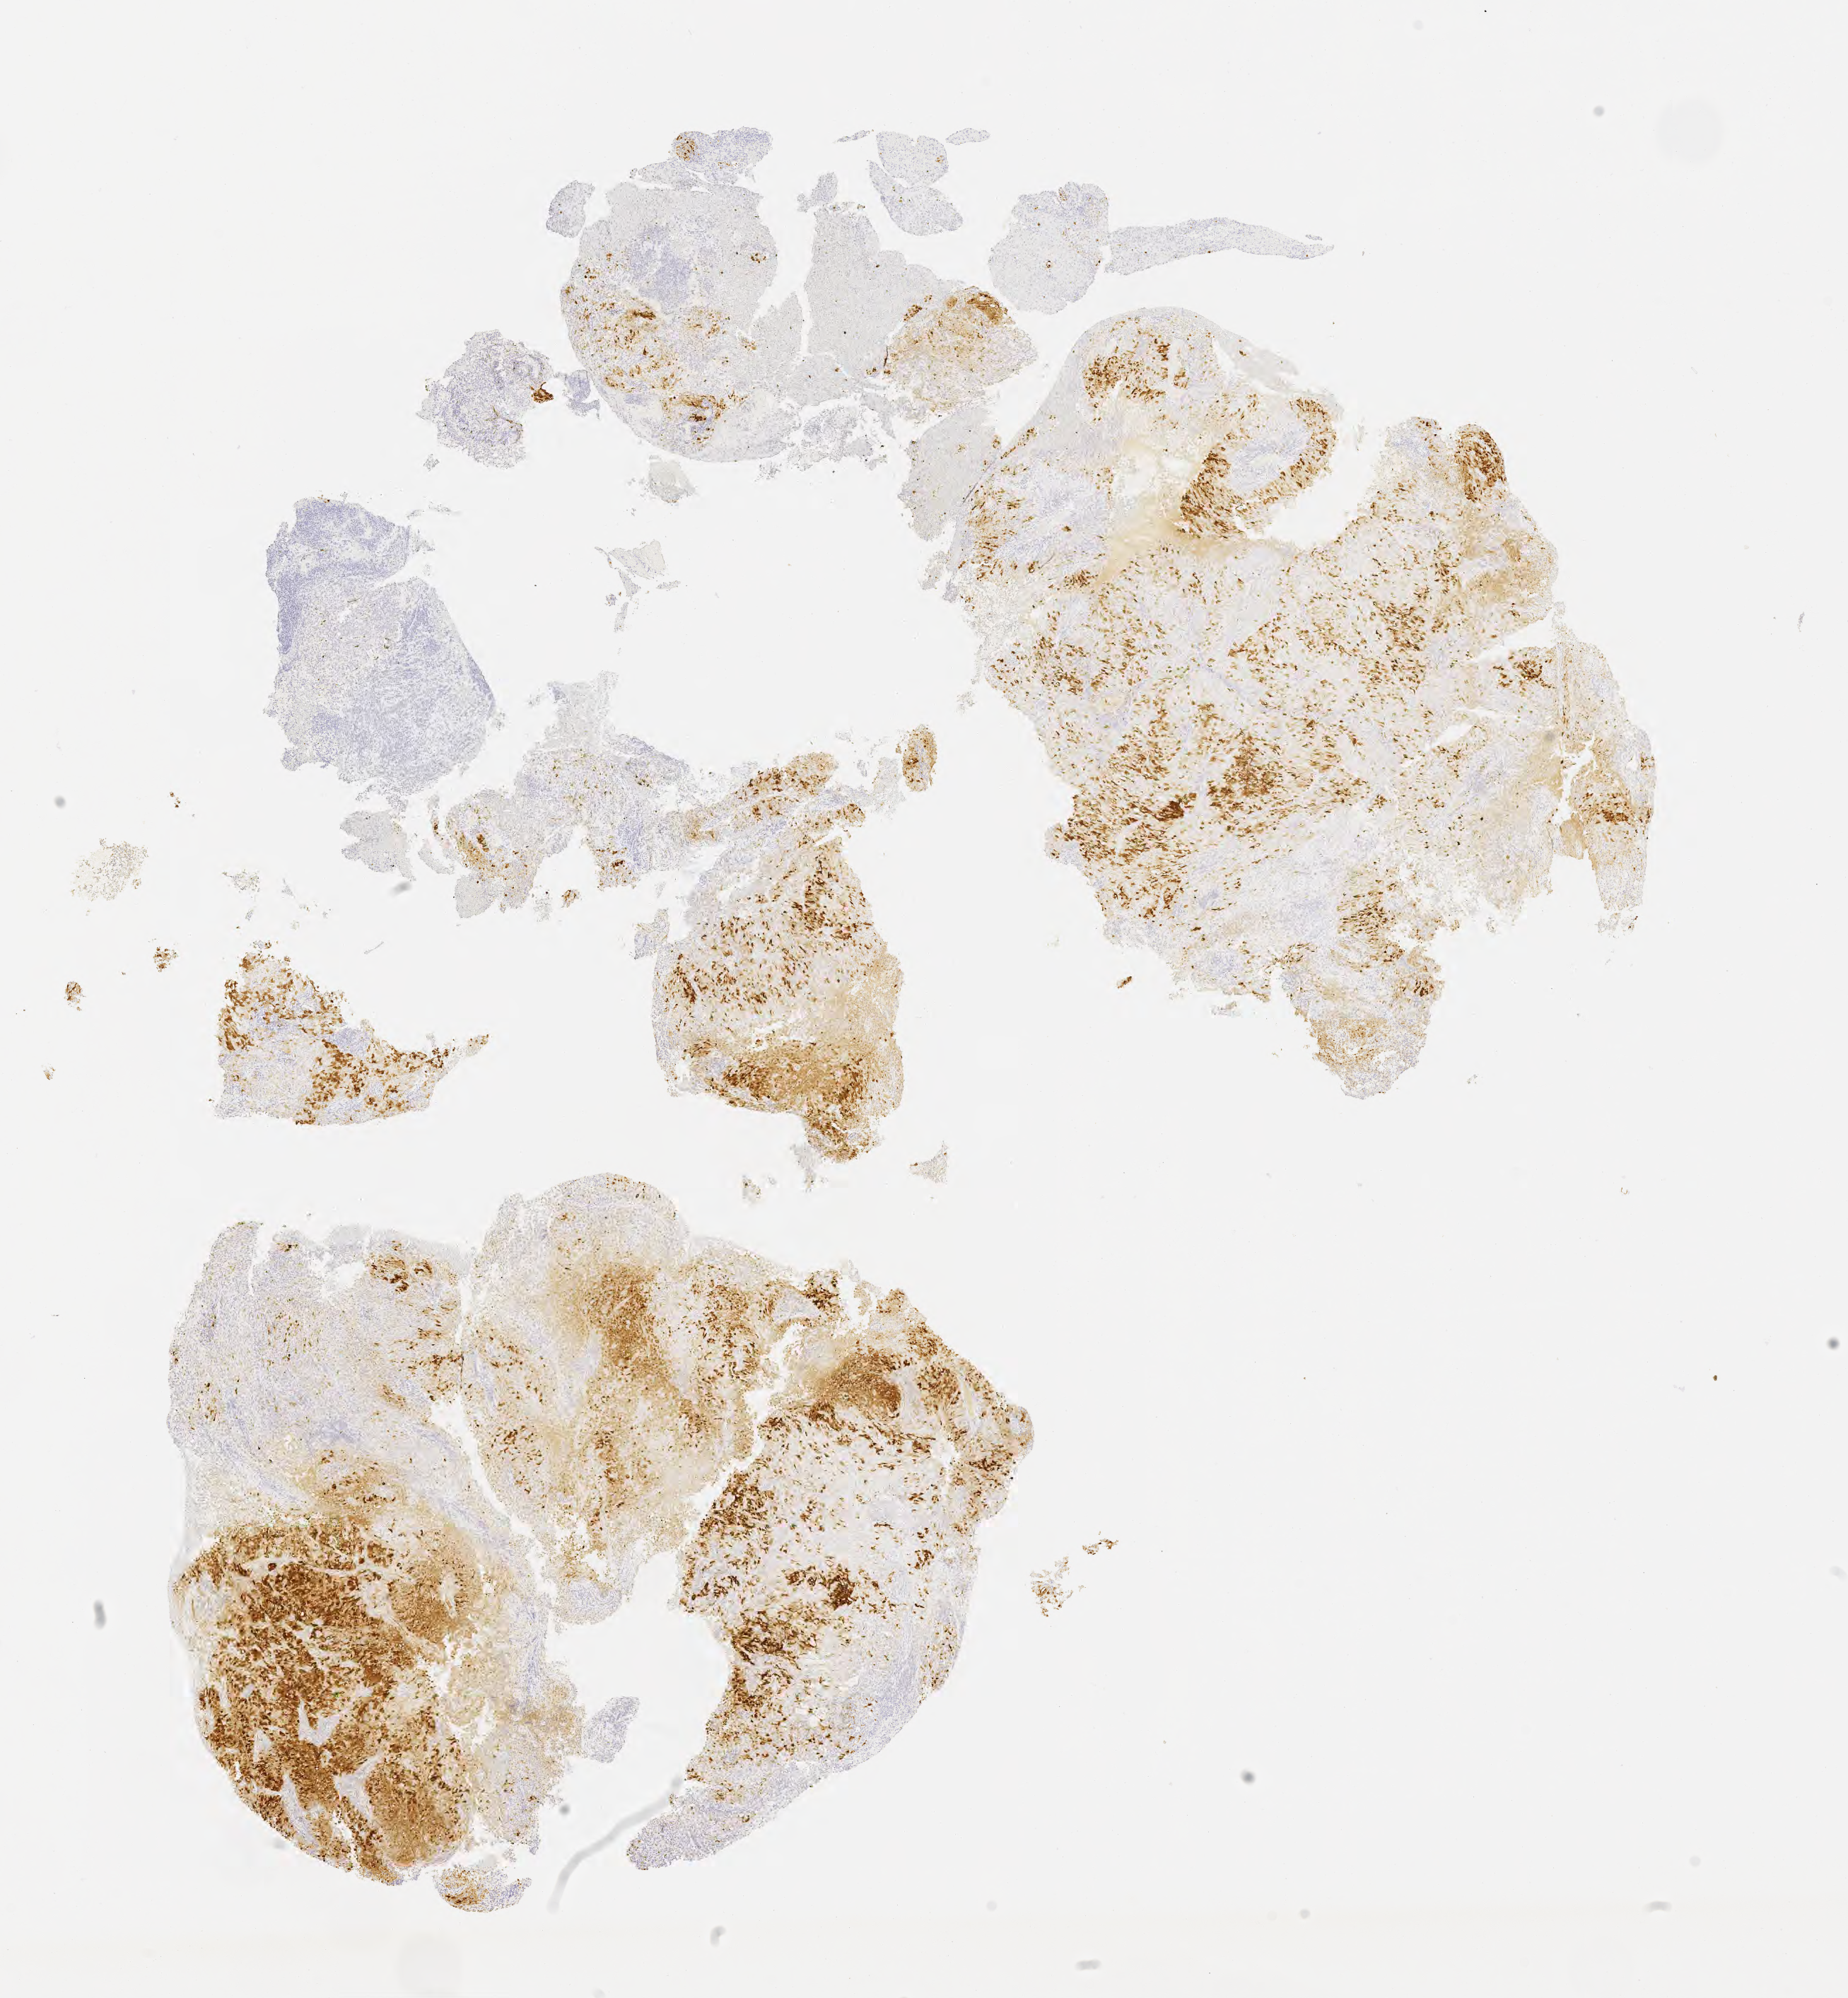
Immunohistochemistry (IHC) whole-slide image stained for p16 (p16INK4a) — low-resolution overview of the scanned area, about 10.6 x 11.4 mm; specimen: tumor tissue; anatomic site: cervix. Patient: female, aged 70.
Diagnosis: Squamous cell carcinoma, large cell, nonkeratinizing, NOS.